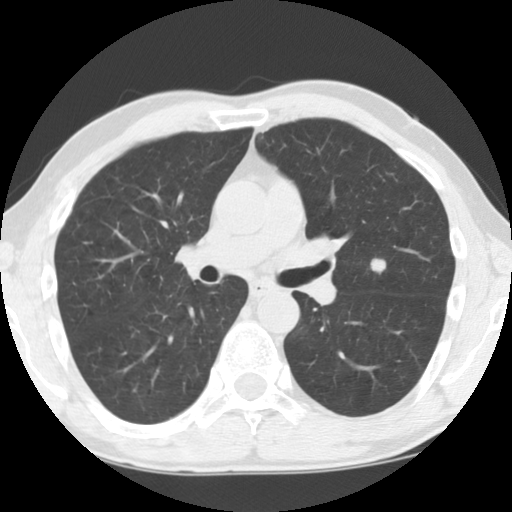
Low-dose screening chest CT, axial slice. Baseline annual screen. Lung window (W 1500 / L -600 HU). Standard (soft-tissue) reconstruction kernel (STANDARD). Slice 116 of 262 in the series. 512 × 512 image matrix, field of view 320 × 320 mm. Male, age 55 years at enrolment. Current smoker at enrolment.
• Expert reader's lesion annotation, bounding box (x1, y1, x2, y2) in pixels: (351, 248, 399, 288).
• The screening reader recorded 5 non-calcified nodules or masses ≥4 mm on this exam; which of them this box marks is not recorded.
• Lung cancer was diagnosed 59 days after this screen: large cell neuroendocrine carcinoma, left upper lobe, stage IA (AJCC 6th edition), 15 mm at pathology.